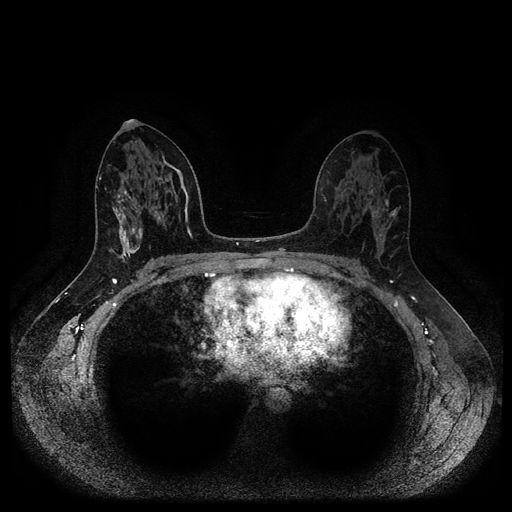
Breast MRI (dynamic contrast-enhanced, multi-phase), one axial slice; position 55 of 116 along the scan axis; dynamic contrast-enhanced series, time point 2 of 5 at this slice position (early post-contrast); 1.5 T; TE 2.6 ms, TR 5.3 ms; 512 × 512 image matrix. Patient: female, 45 years.
Annotated regions visible in this slice (semi-automatically segmented with operator editing):
- breast lesion (labelled benign in the annotation): box from (x=112, y=205) to (x=143, y=264) px